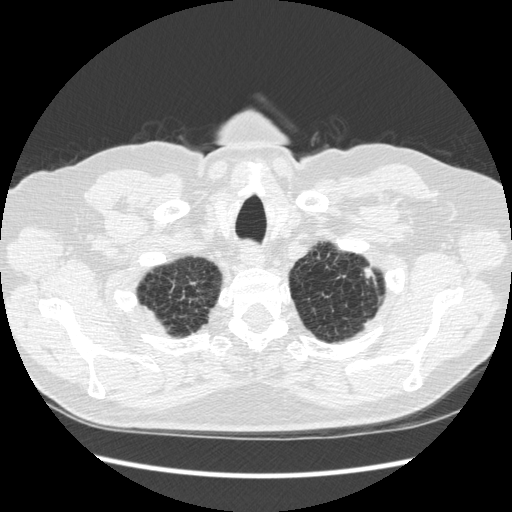
Low-dose screening chest CT, one axial slice; position 247 of 267 along the scan axis; lung window (W 1500 / L -600 HU); 512 × 512 image matrix.
Annotated regions visible in this slice (outlined manually by an expert reader):
- lesion 1 (tumor, upper lobe of left lung): bounding box (x1, y1, x2, y2) in pixels: (364, 268, 376, 284)